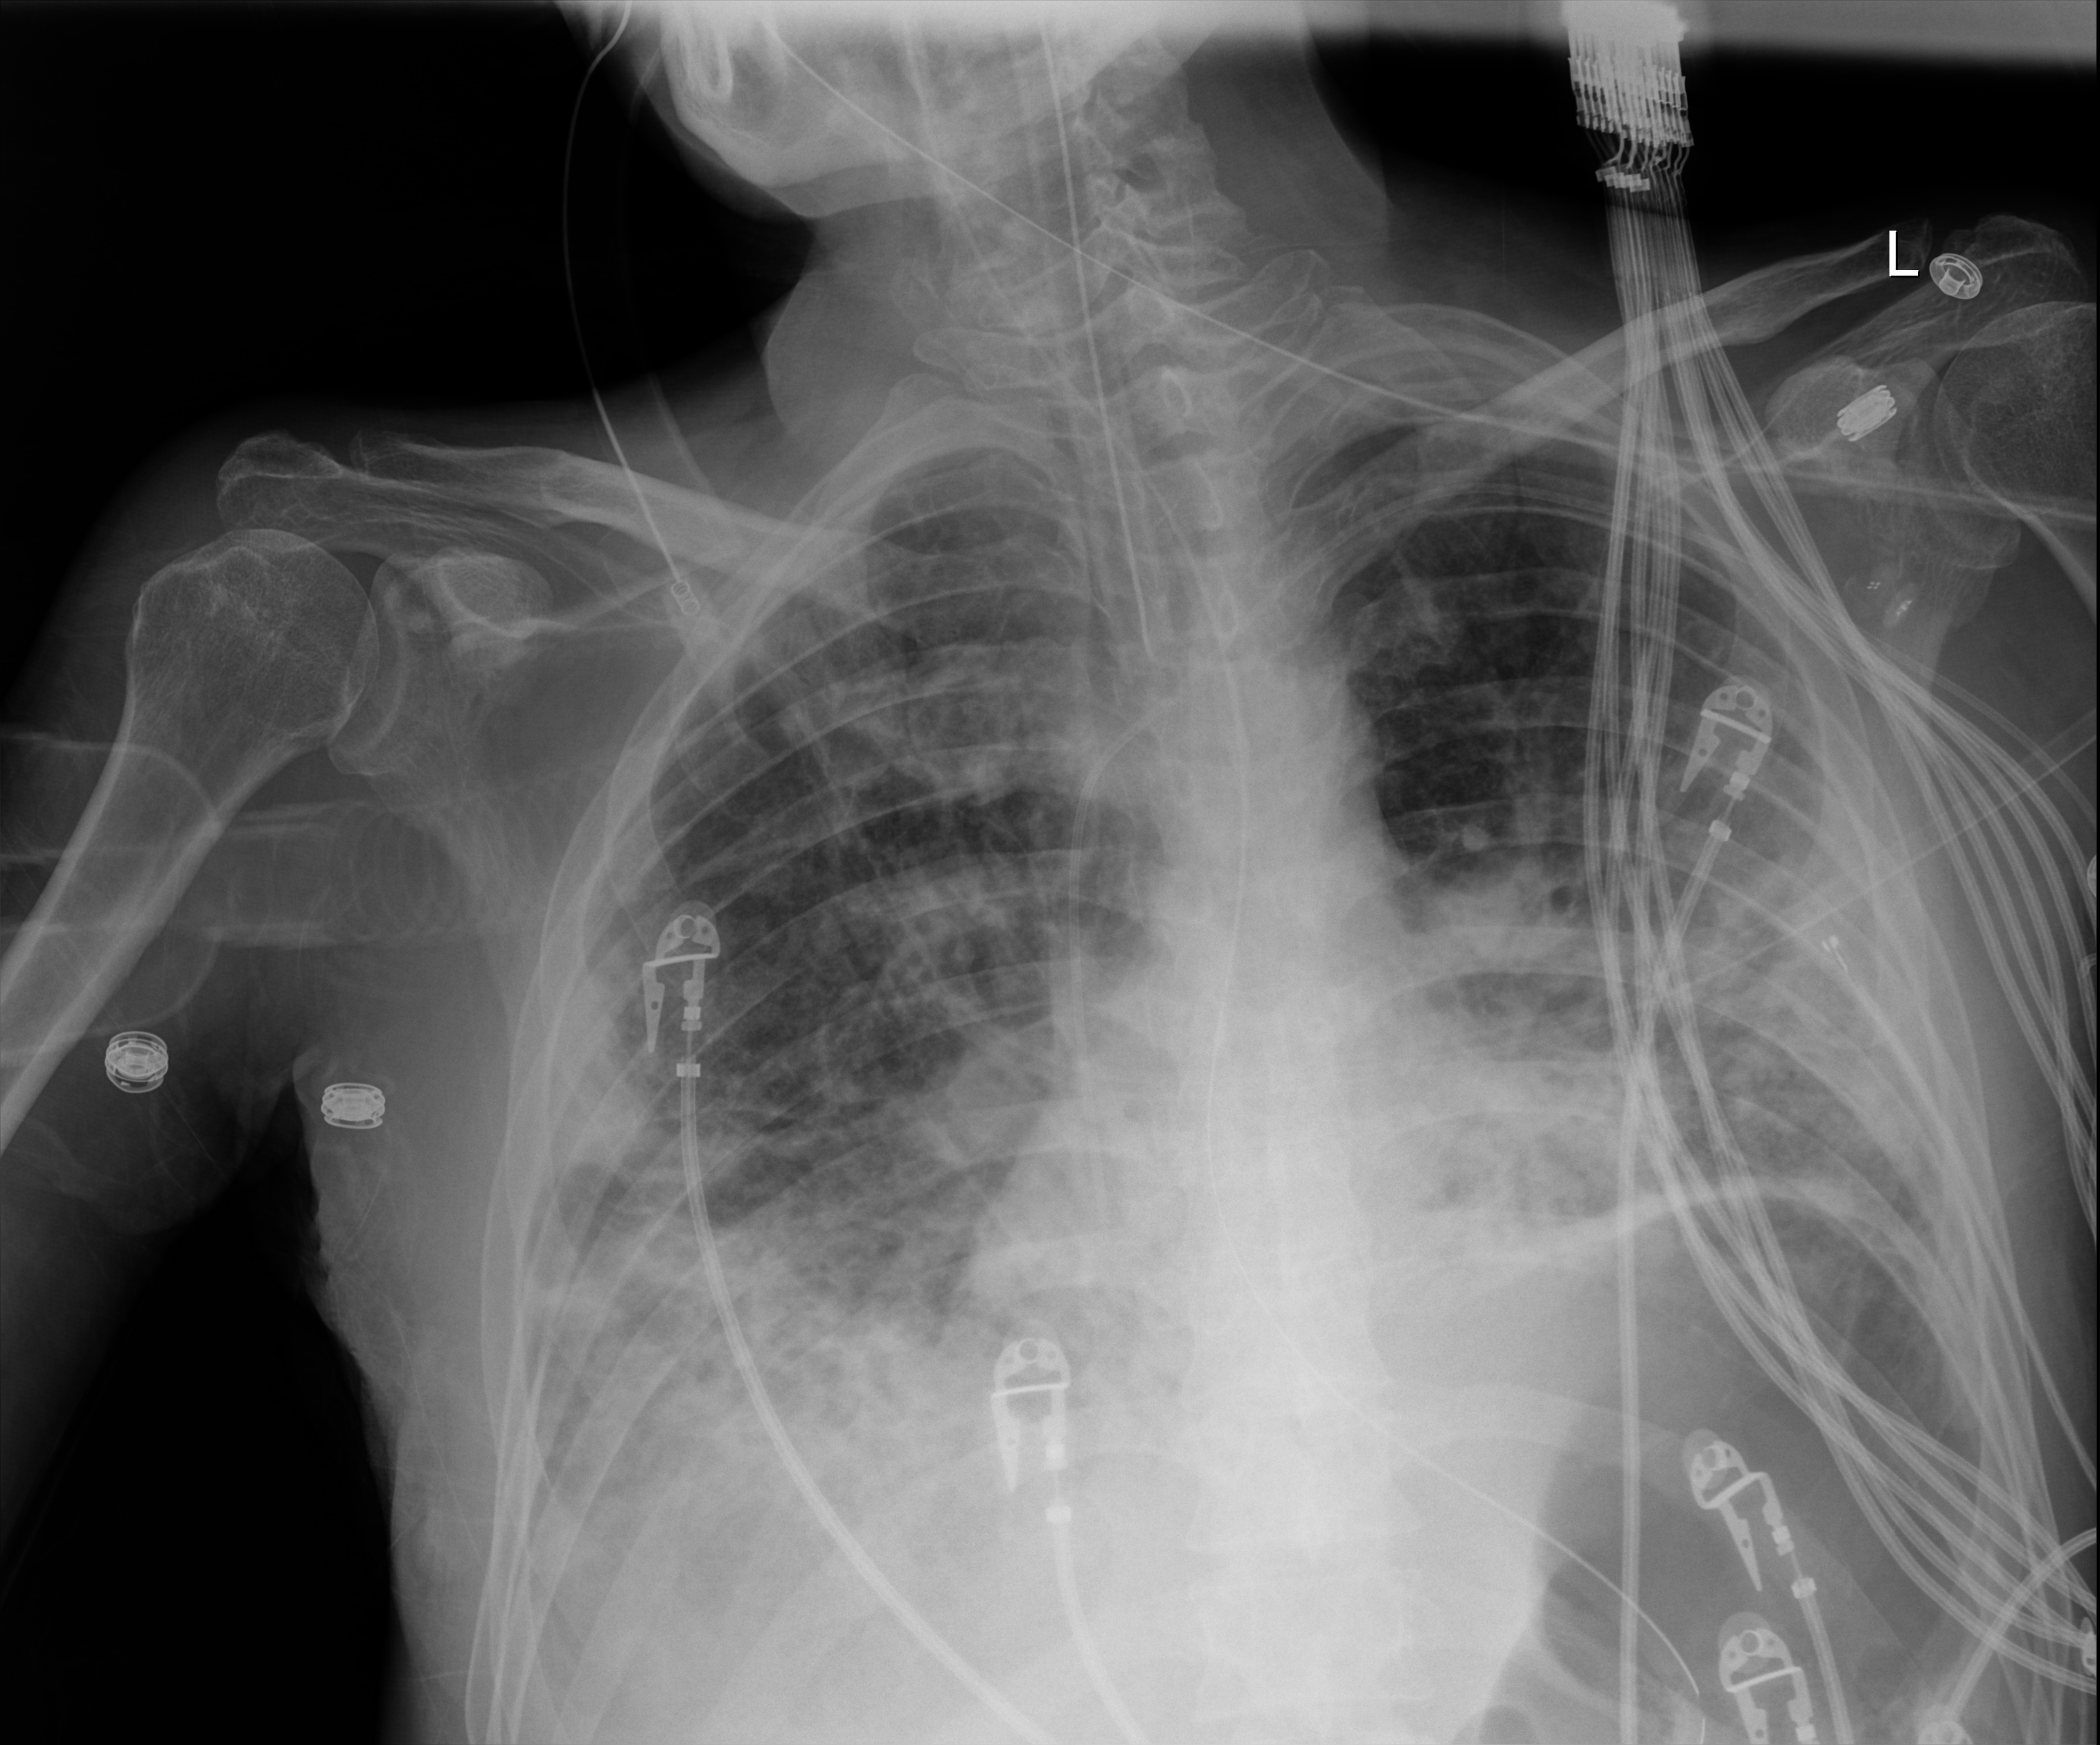
Chest radiograph (digital radiography), anteroposterior (AP) projection. Patient hospitalised with COVID-19; male, aged 18–59 years.
Hospital-stay facts (about this admission, not read from this image; timing relative to this image not recorded): mechanically ventilated during this hospital stay: yes; admitted to intensive care during this hospital stay: yes.